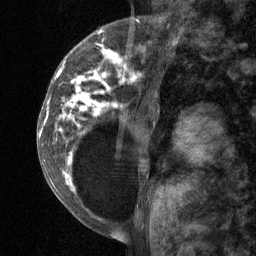
Breast MRI (dynamic contrast-enhanced), one sagittal slice; dynamic contrast-enhanced study with each time point stored as its own series, time point 2 of 3 at this slice position (early post-contrast, ordered by acquisition time); 1.5 T; TE 4.8 ms, TR 27 ms; 2 mm slice thickness; 256 × 256 image matrix, field of view 180 × 180 mm. Patient: female, 34 years. Case-level facts recorded for this patient, not image findings: setting: breast cancer imaged before/during neoadjuvant chemotherapy; receptor status: HR-positive, HER2-negative.
Outlined on this slice (semi-automatic segmentation, software-assisted and operator-edited):
- analysis volume of interest (the breast-tissue region the enhancement analysis was run in; not a lesion): bounding box [x1, y1, x2, y2] px = [41, 23, 157, 197]
- tumour enhancement mask (voxels above the 90 % enhancement threshold inside the analysis volume of interest): [44, 30, 142, 191]